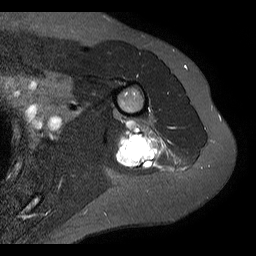
MRI of an extremity soft-tissue mass, one axial slice. Position 6 of 20 along the scan axis. STIR. 4 mm slice thickness. 256 × 256 image matrix. Female patient. Case-level facts recorded for this patient, not image findings: histological type: malignant fibrous histiocytoma; grade: low; site of the primary tumour: left arm.
Annotated regions visible in this slice (expert manual segmentation):
- gross tumour volume (mass): bounding box (x1, y1, x2, y2) in pixels: (116, 120, 167, 171)